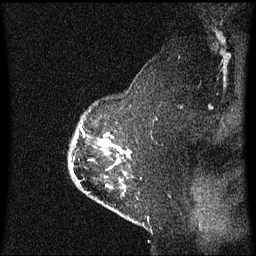
Breast MRI (dynamic contrast-enhanced), one sagittal slice; position 47 of 60 along the scan axis; dynamic contrast-enhanced series, image 2 of 3 at this slice position (ordered by acquisition); 1.5 T; TE 4.2 ms, TR 8.4 ms; 2 mm slice thickness; 256 × 256 image matrix, field of view 210 × 210 mm. Patient: female, 54 years. From the clinical record (not read from this slice): setting: breast cancer imaged before/during neoadjuvant chemotherapy; receptor status: HER2-positive.
Structures marked on this image (semi-automatically segmented with operator editing):
- analysis volume of interest (the breast-tissue region the enhancement analysis was run in; not a lesion): bounding box <72,122,132,196> (left, top, right, bottom; pixels)
- tumour enhancement mask (voxels above the 70 % enhancement threshold inside the analysis volume of interest): <108,142,122,151>